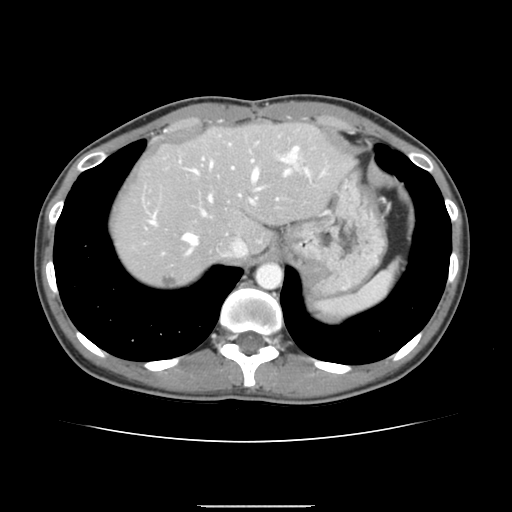
Contrast-enhanced abdominal CT, one axial slice. Position 118 of 150 along the scan axis. 120 kVp. Intravenous contrast given. Soft-tissue window (W 400 / L 40 HU). 2.5 mm slice thickness. 512 × 512 image matrix, field of view 324 × 324 mm. Female patient, age 32 years. Case-level facts recorded for this patient, not image findings: diagnosis: colorectal cancer liver metastases, imaged before liver resection; multiple liver metastases: yes; largest metastasis: 0.7 cm; chemotherapy before resection: yes.
Annotated regions visible in this slice (manually delineated by an expert):
- hepatic veins: bounding box <150,154,297,256> (left, top, right, bottom; pixels)
- liver: <113,124,351,287>
- planned liver remnant (the part of the liver to remain after resection): <113,124,351,260>
- portal vein (with intrahepatic branches): <202,146,325,215>
- liver metastasis: <161,274,177,286>